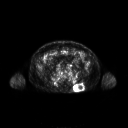
FDG PET of an extremity soft-tissue mass (from a PET/CT study), one axial slice. Position 90 of 267 along the scan axis. 128 × 128 image matrix, field of view 700 × 700 mm. Patient: male, 61 years. From the clinical record (not read from this slice): histological type: pleiomorphic leiomyosarcoma; grade: high; site of the primary tumour: left buttock.
Annotated regions visible in this slice (expert contour drawn on MRI and transferred to this co-registered scan by the dataset authors):
- gross tumour volume including surrounding oedema: bounding box (x1, y1, x2, y2) in pixels: (73, 83, 84, 92)
- gross tumour volume (mass): (73, 84, 84, 92)